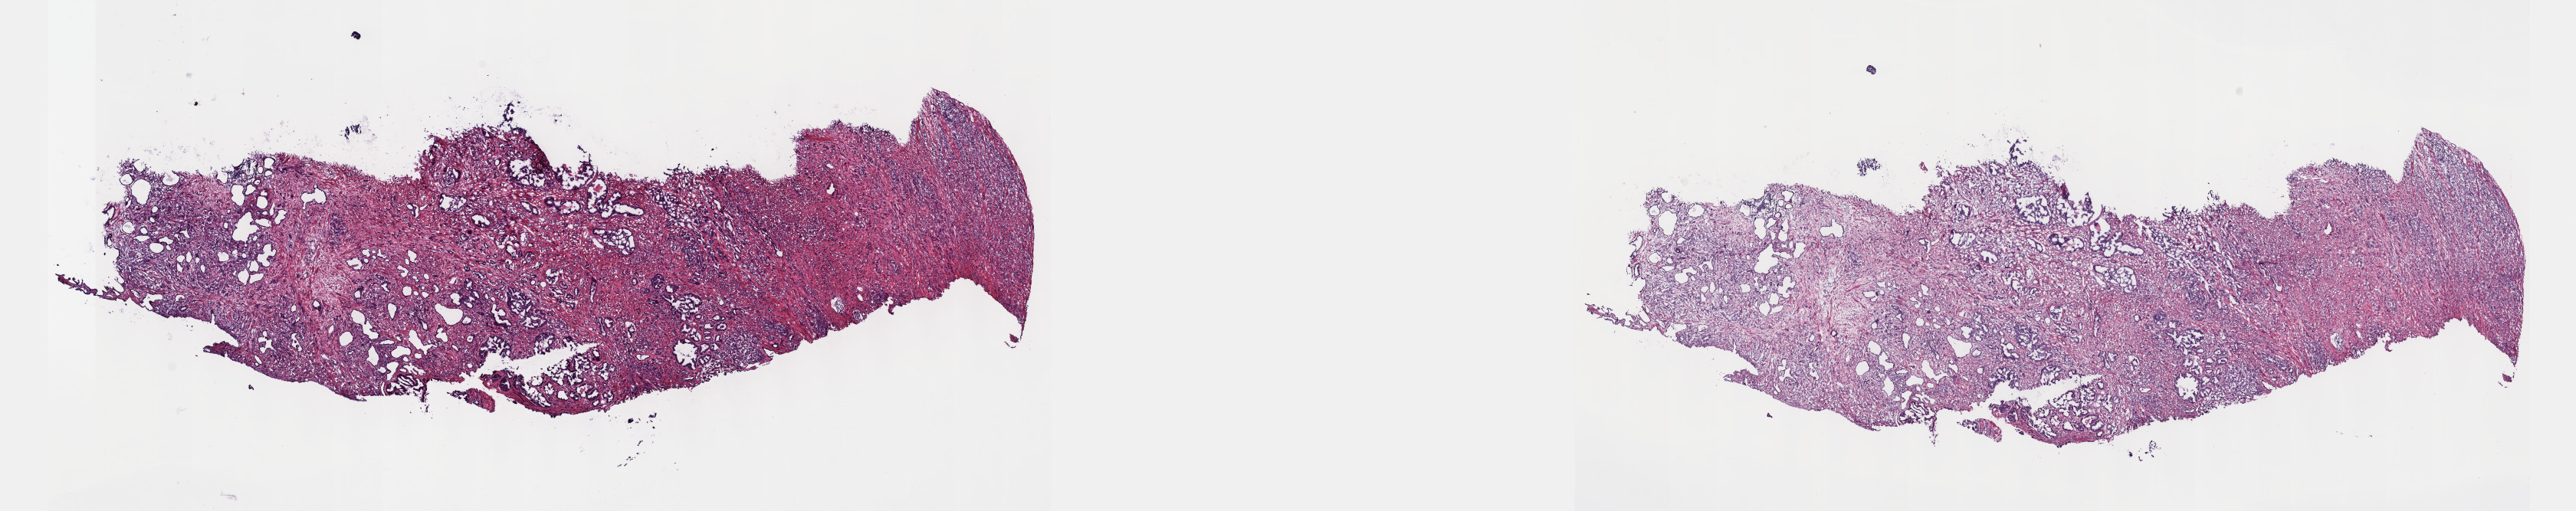
H&E whole-slide image, whole scanned area (about 27.2 x 5.4 mm) shown as a low-resolution overview; frozen section; sample: primary tumour, prostate. Patient: male, age at initial diagnosis 63 years. Gleason score: 8 (4+4). Pathologist review of this section (percent, as recorded): tumour cells 70%, tumour nuclei 70%, normal cells 10%, stromal cells 20%, necrosis 0%. Inflammatory infiltration, as recorded: lymphocyte infiltration 2%, monocyte infiltration 0%, neutrophil infiltration 0%.
Laterality: right. Diagnosis: Adenocarcinoma, NOS (prostate gland).